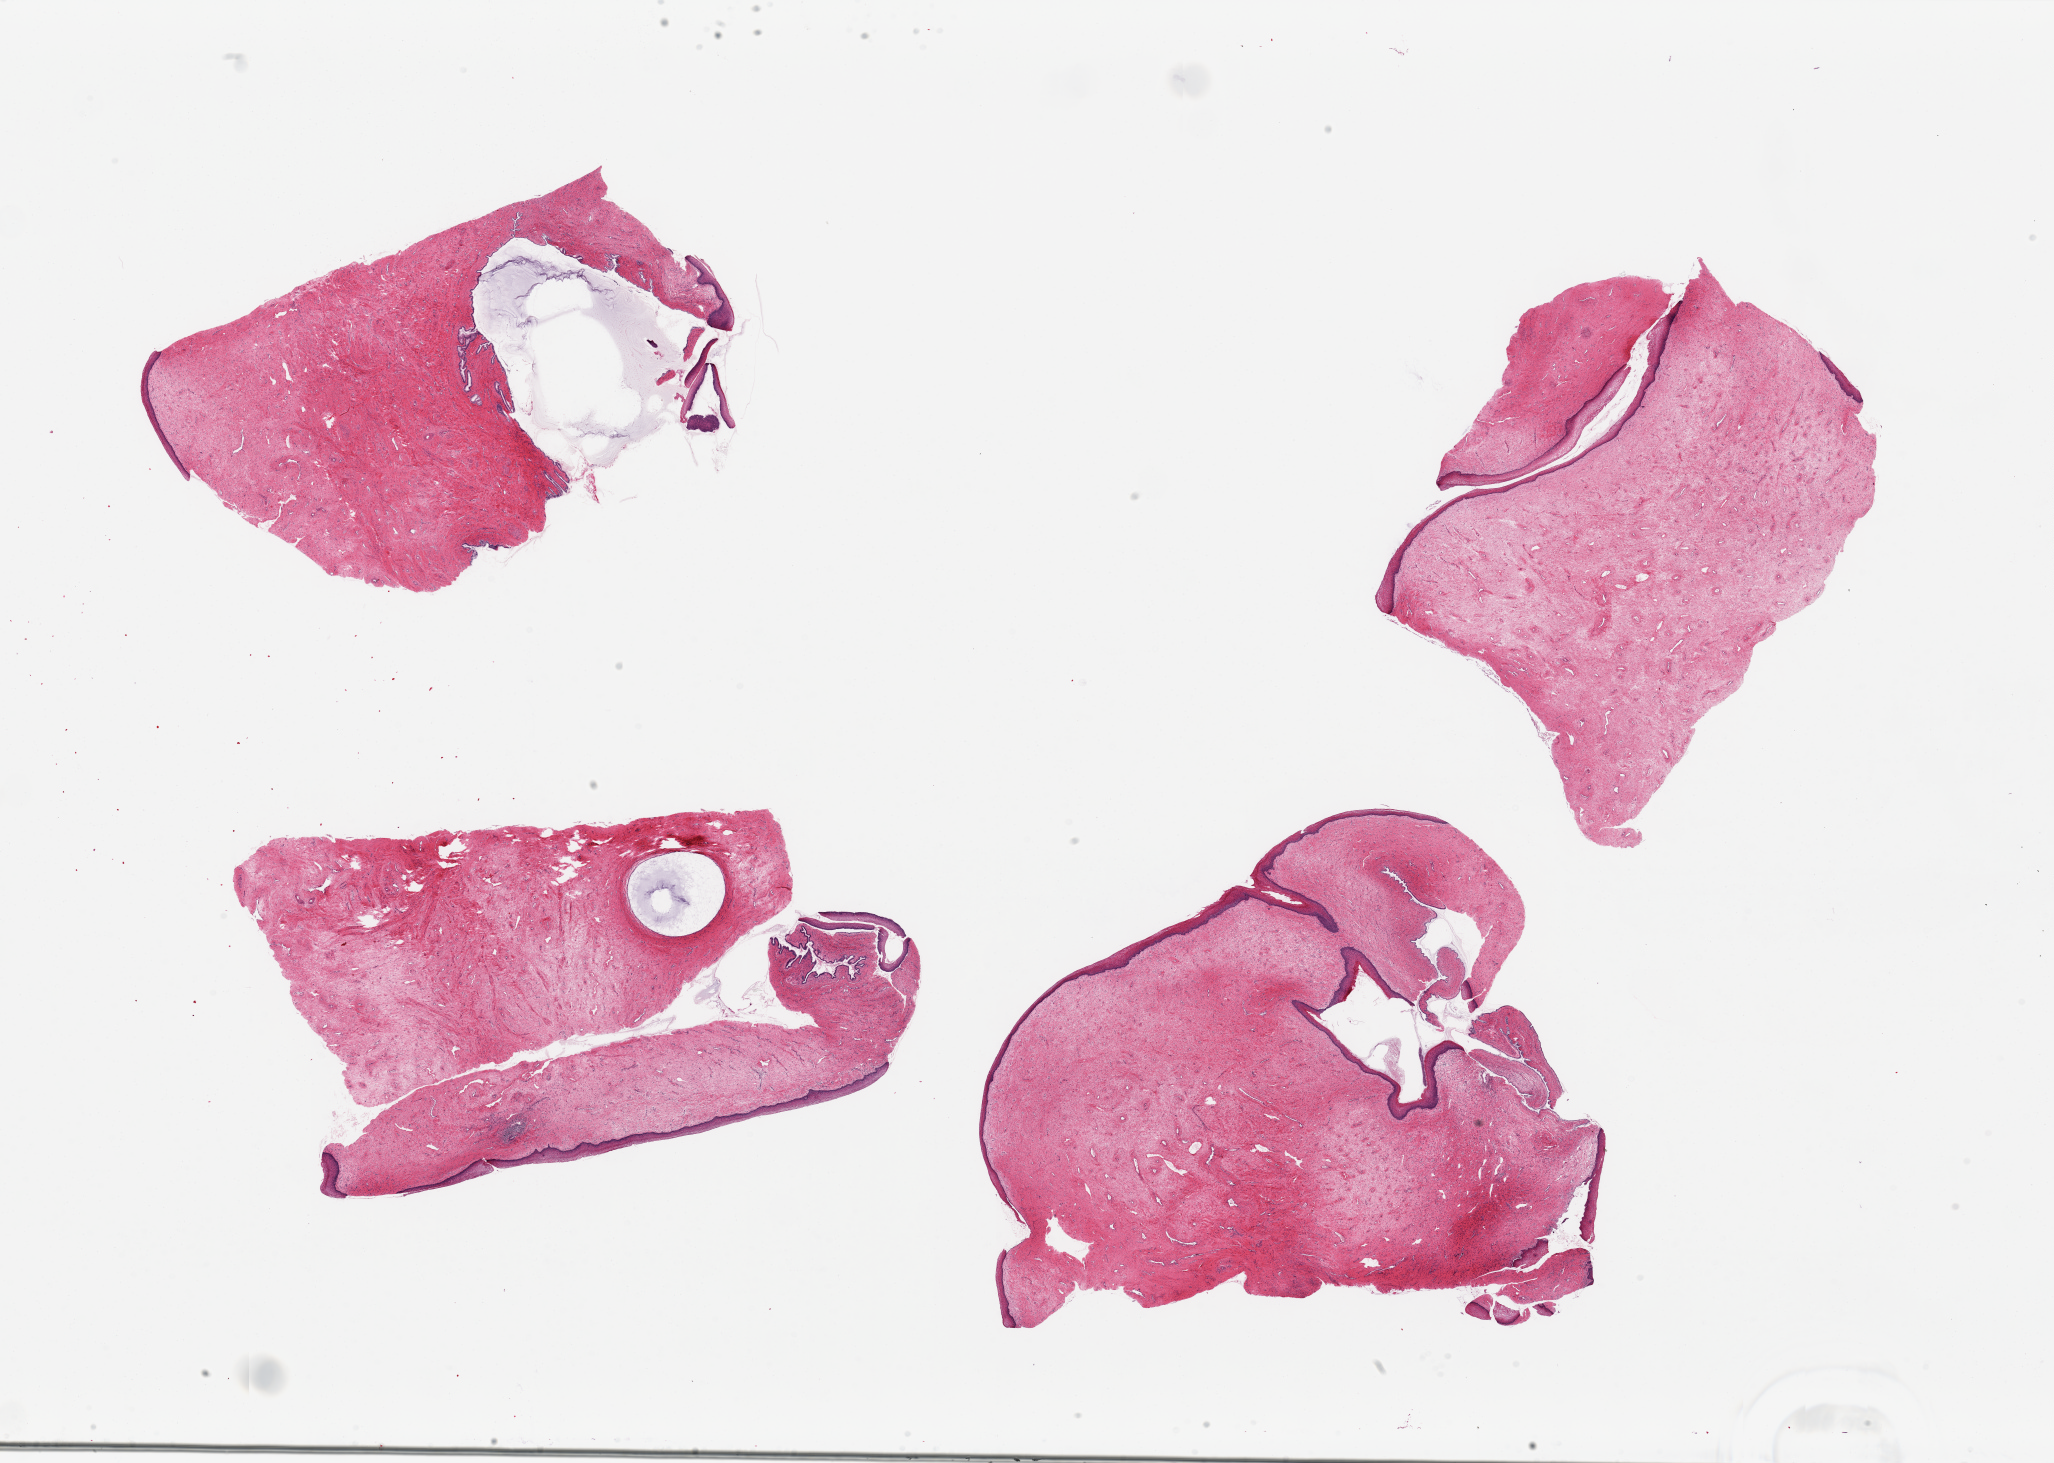
Digitized H&E-stained section — whole scanned area (about 32.5 x 23.1 mm) shown as a low-resolution overview, PAXgene-fixed, paraffin-embedded tissue, target tissue: exocervix, tissue donor sample.
Review note (as recorded): 4 pieces ~8x5mm. Ectocervix present on all, ~3-5% of thickness; Nabothian cysts and endocervical mucoa present in 2.